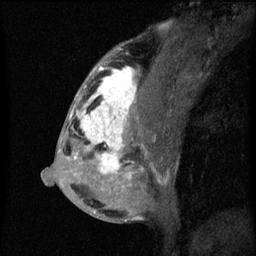
Breast MRI (dynamic contrast-enhanced), one sagittal slice. Position 29 of 60 along the scan axis. Dynamic contrast-enhanced series, image 2 of 3 at this slice position (ordered by acquisition). 1.5 T. TE 4.2 ms, TR 8 ms. 2 mm slice thickness. 256 × 256 image matrix, field of view 180 × 180 mm. Patient: female, 50 years.
Outlined on this slice (semi-automatically segmented with operator editing):
- analysis volume of interest (the breast-tissue region the enhancement analysis was run in; not a lesion): box from (x=66, y=64) to (x=141, y=187) px
- tumour enhancement mask (voxels above the 70 % enhancement threshold inside the analysis volume of interest): (x=69, y=66)–(x=137, y=181)